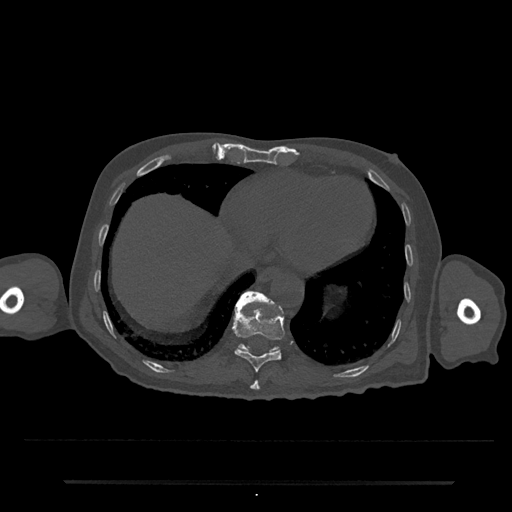
CT including the spine, one axial slice. Position 301 of 797 along the scan axis. Bone window (W 1800 / L 400 HU). 0.5 mm slice thickness. 512 × 512 image matrix. Patient: male, 74 years. From the clinical record (not read from this slice): primary cancer: prostate.
Outlined on this slice (semi-automatically segmented with operator editing):
- T10 vertebra: box from (x=232, y=306) to (x=285, y=372) px
- T11 vertebra: (x=235, y=291)–(x=280, y=352)
- T9 vertebra: (x=250, y=380)–(x=260, y=391)